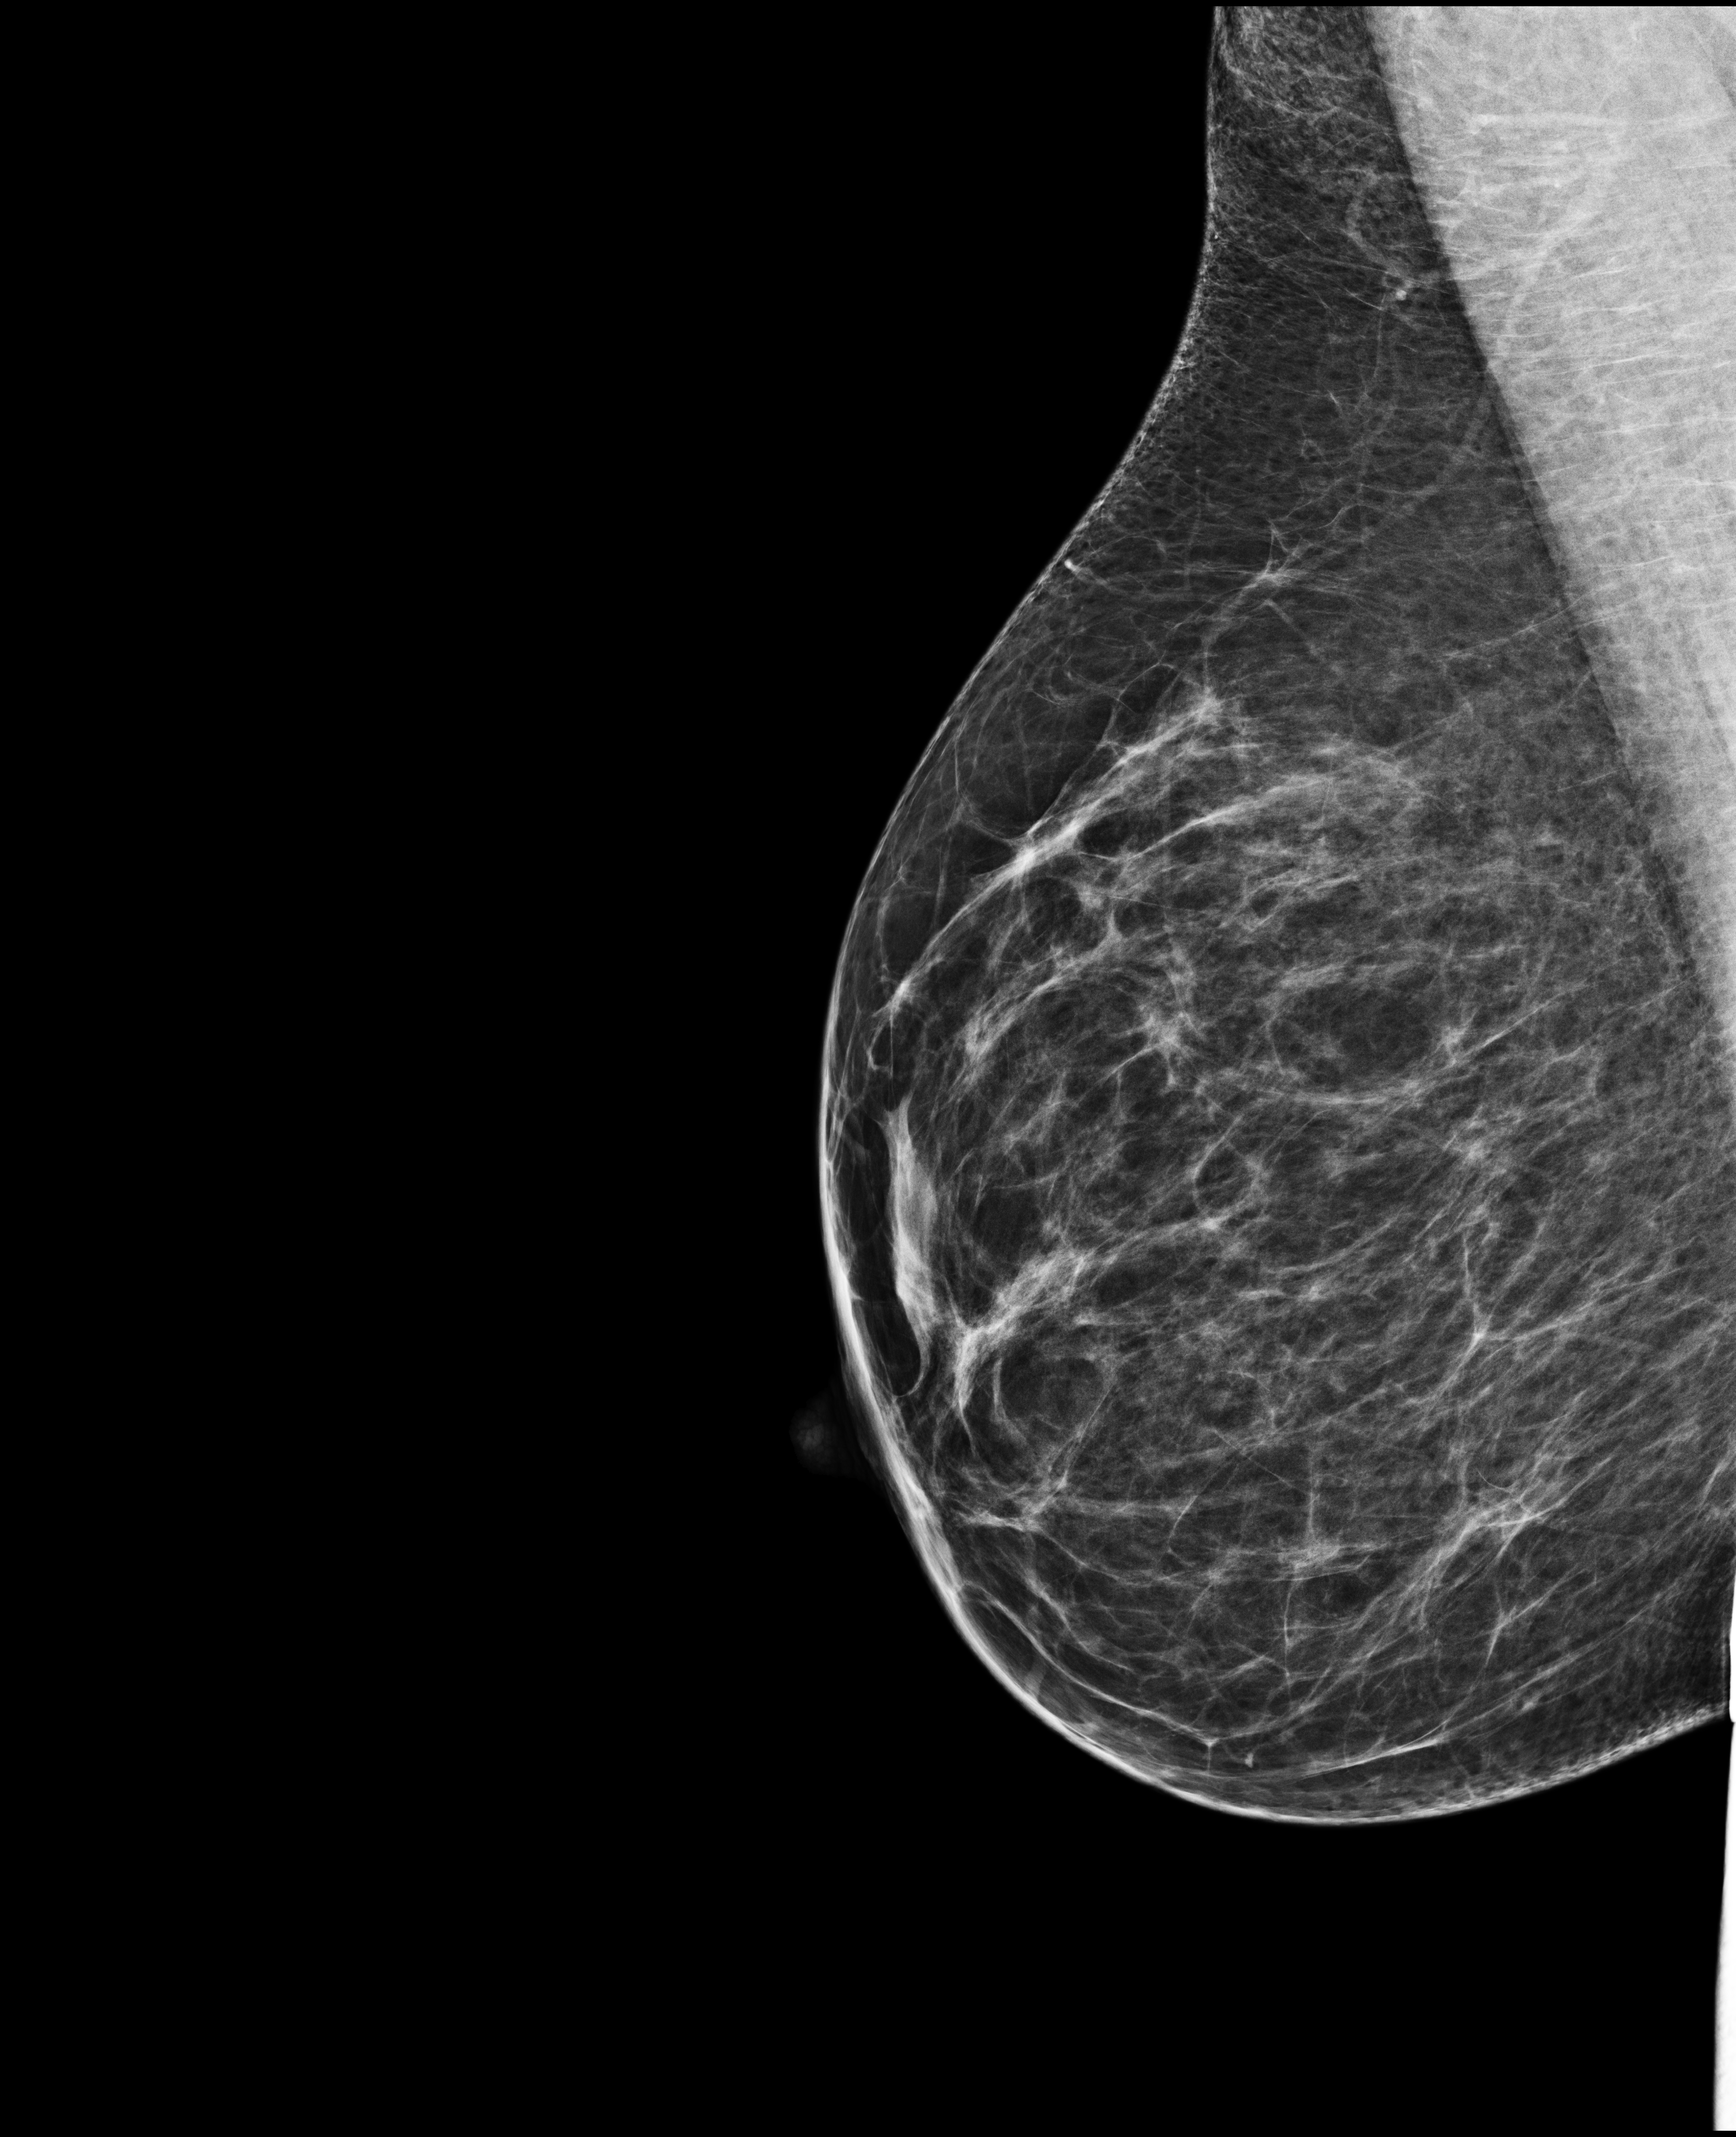
Screening examination; system: Selenia Dimensions. Patient aged 42 years (female).
Image type: full-field digital mammogram. Breast: right. Projection: mediolateral oblique (MLO) view.